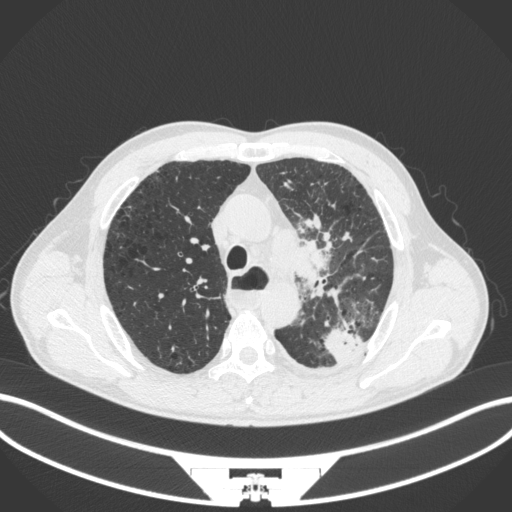
Chest CT, one axial slice; slice 281 of 411 in the series (ordered by position); reconstruction kernel B31f; 120 kVp; lung window (W 1500 / L -600 HU); 1 mm slice thickness; 512 × 512 image matrix, field of view 400 × 400 mm. Patient: male, 57 years. From the clinical record (not read from this slice): clinical TNM (as recorded): T2a N1 M0.
Annotated regions visible in this slice (bounding box drawn by a radiologist):
- lung tumour (recorded histology: squamous cell carcinoma): box from (x=285, y=230) to (x=340, y=300) px